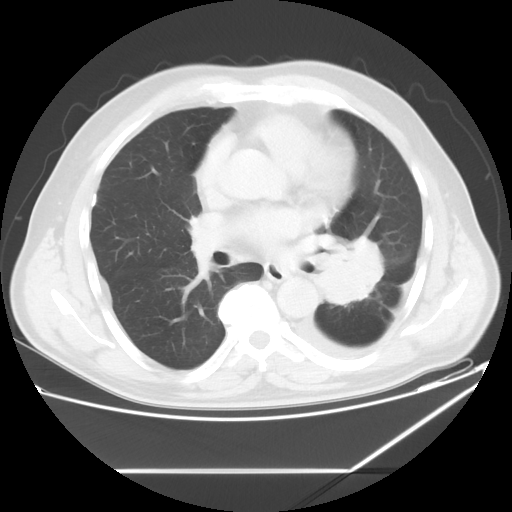
Chest CT, one axial slice. Position 31 of 60 along the scan axis. 120 kVp. Lung window (W 1500 / L -600 HU). 5 mm slice thickness. 512 × 512 image matrix, field of view 395 × 395 mm. Male patient, age 62 years. Case-level facts recorded for this patient, not image findings: clinical TNM (as recorded): T3 N0 M1.
Outlined on this slice (rectangle marked by the reading radiologist):
- lung tumour (recorded histology: adenocarcinoma): bounding box [x1, y1, x2, y2] px = [311, 233, 389, 311]
- lung tumour (recorded histology: adenocarcinoma): [320, 233, 385, 307]